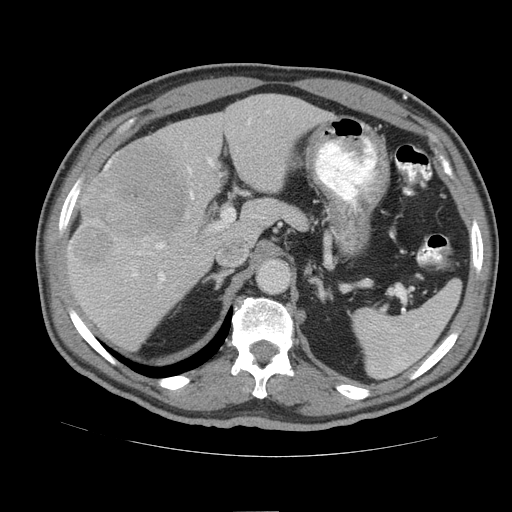
Contrast-enhanced abdominal CT (liver protocol), one axial slice. Slice 58 of 105 in the series (ordered by position). Reconstruction kernel STANDARD. 140 kVp. Soft-tissue window (W 400 / L 40 HU). 2.5 mm slice thickness. 512 × 512 image matrix, field of view 380 × 380 mm. From the clinical record (not read from this slice): diagnosis: hepatocellular carcinoma (patient treated with transarterial chemoembolisation; whether this scan precedes or follows treatment is not stated here); TNM stage (as recorded): Stage-IIIB; Child-Pugh class: A; tumour nodularity: multinodular.
Structures marked on this image (semi-automatic segmentation, software-assisted and operator-edited):
- liver parenchyma outside the tumour (the mass and vessels are separate outlines, so this box may not span the whole liver): box from (x=66, y=94) to (x=333, y=350) px
- mass: (x=75, y=144)–(x=187, y=265)
- liver vessels: (x=69, y=120)–(x=250, y=281)